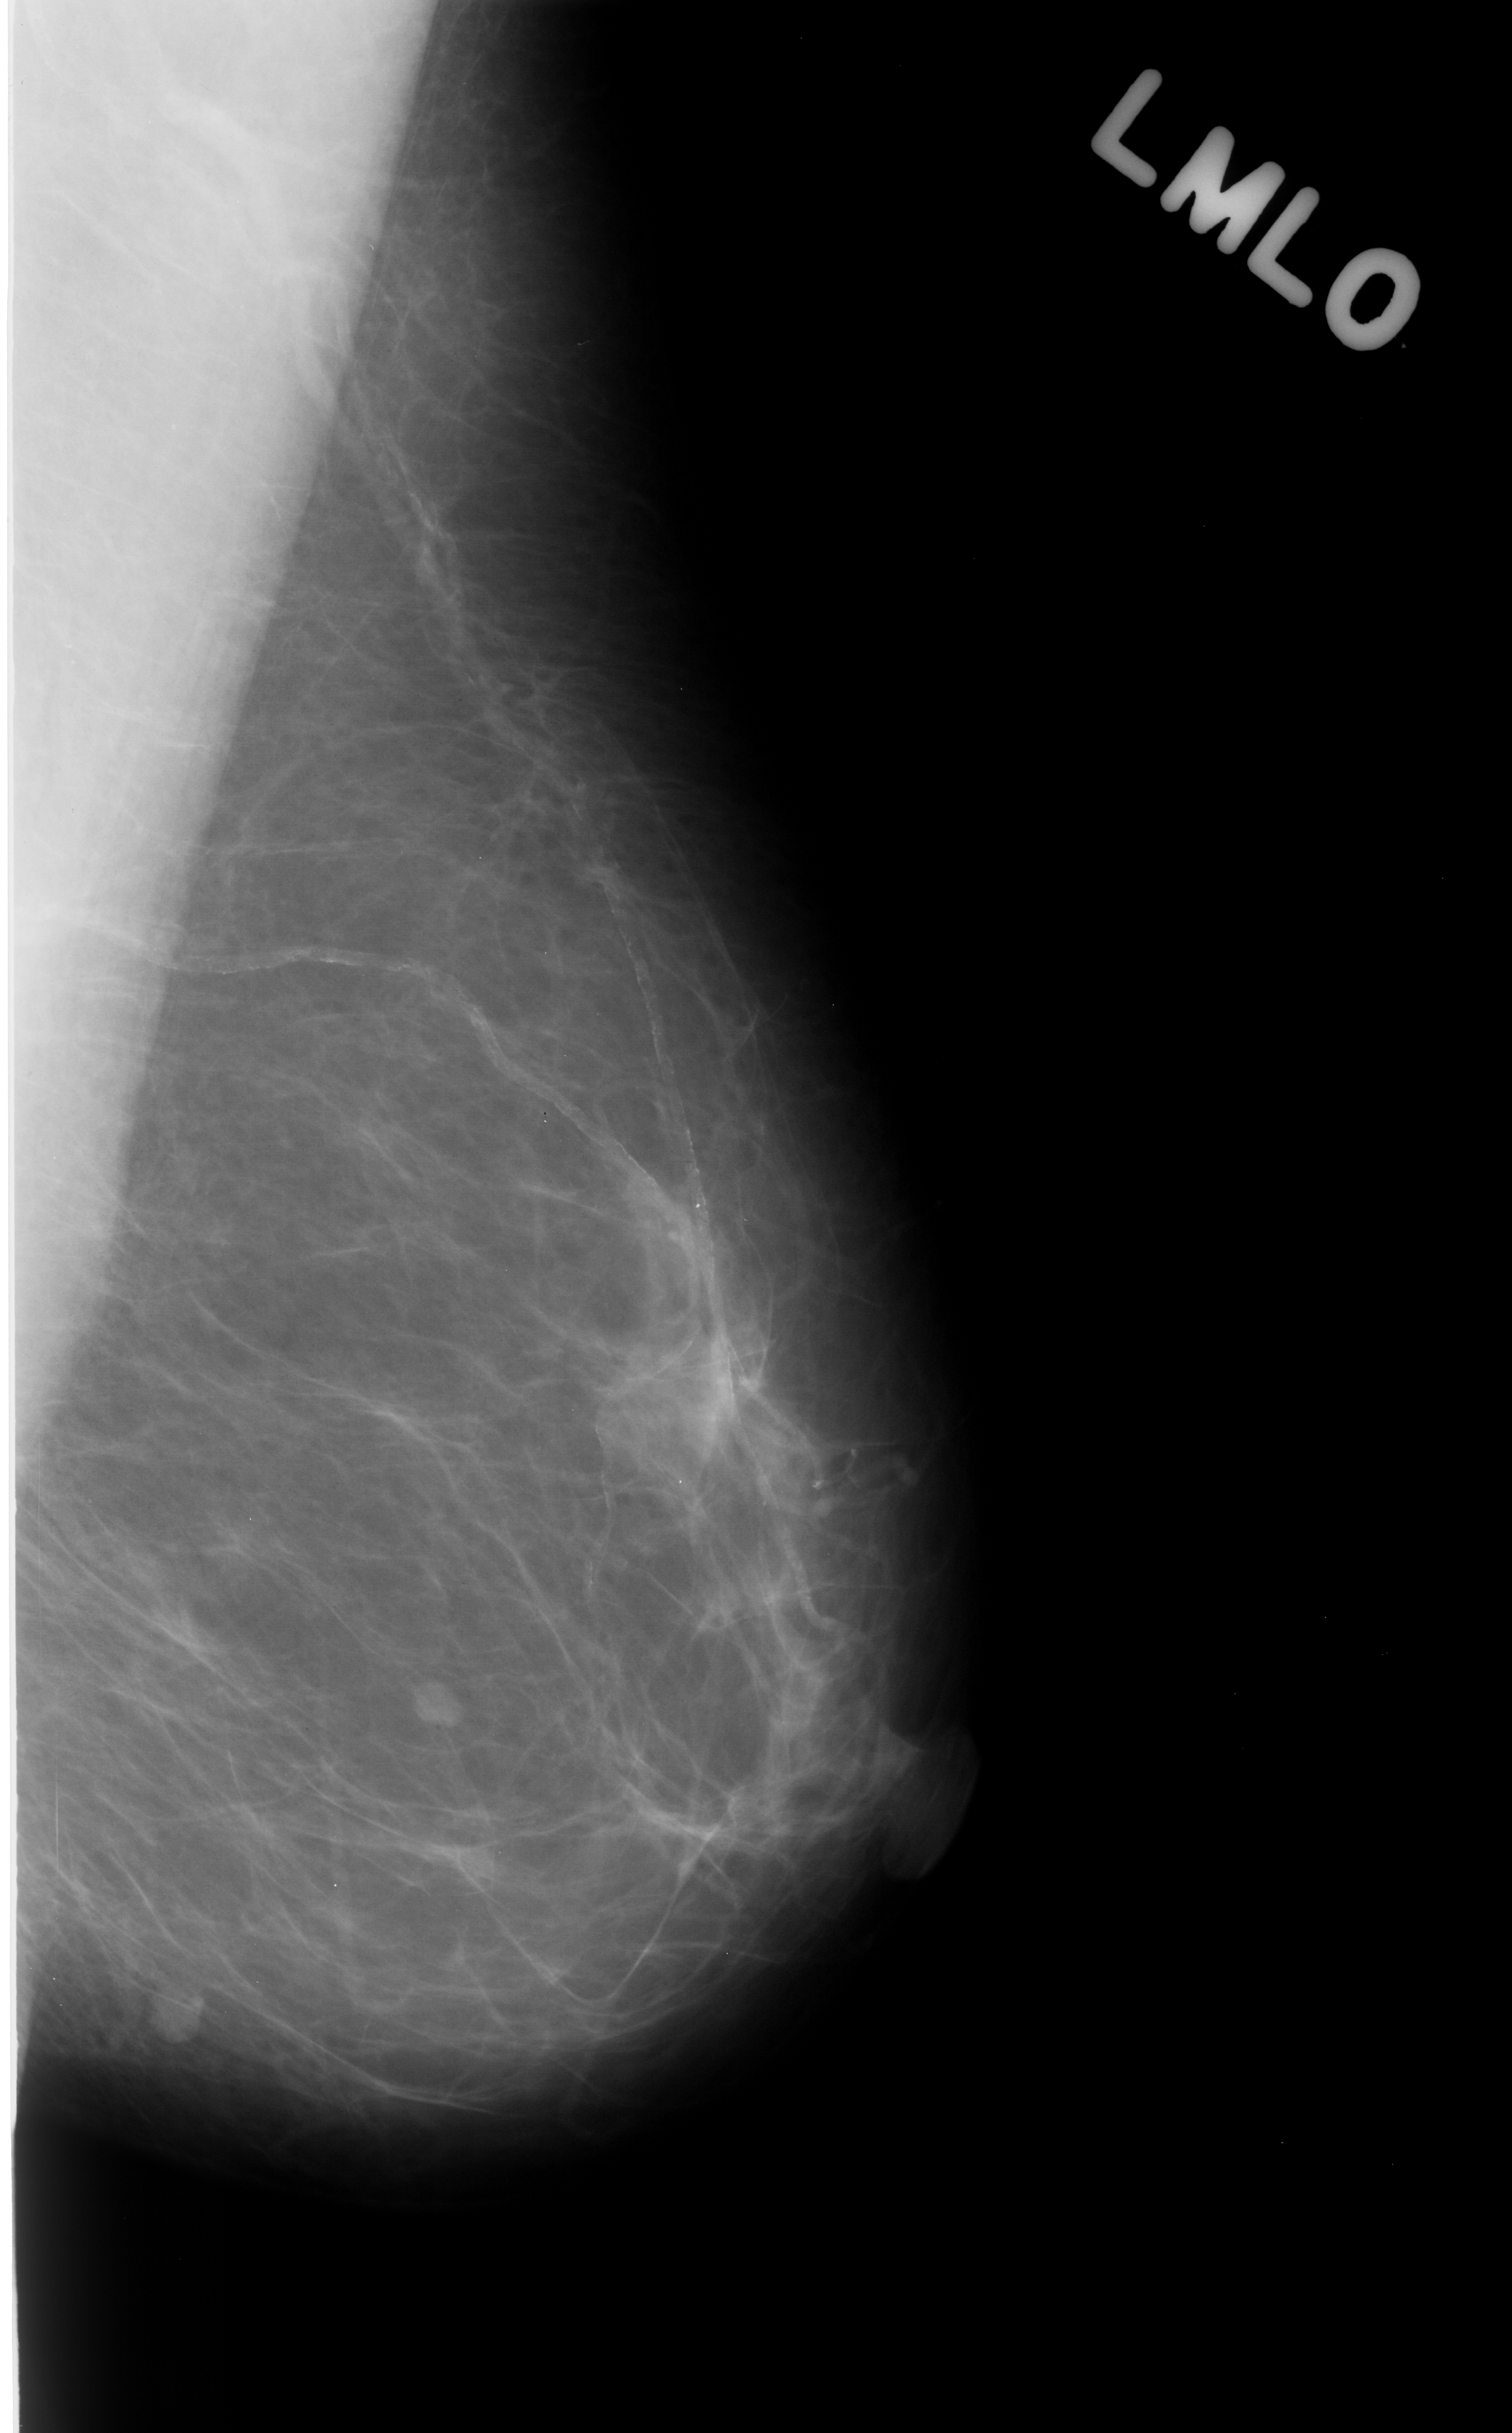
Mammogram (digitized film); left breast; MLO view; BI-RADS breast density category 1 (scale 1–4); 1512 × 2433 image matrix.
Expert-marked regions of interest on this film, with their recorded descriptors:
- mass, shape lobulated, margins circumscribed; BI-RADS assessment category 3; subtlety rating 5 on a 1 (subtle) to 5 (obvious) scale; pathology result (as recorded, not read from the image): benign: bounding box [x1, y1, x2, y2] px = [392, 1662, 486, 1750]